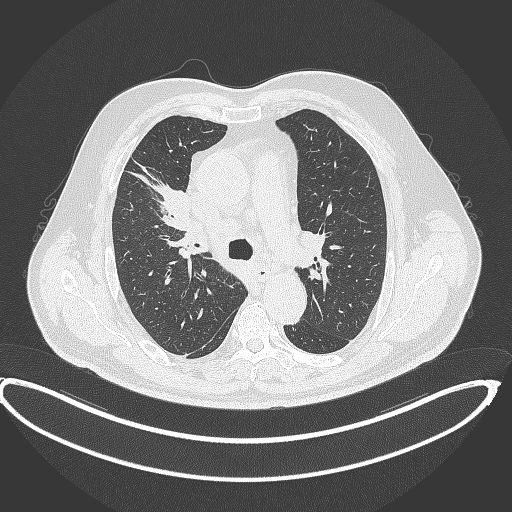
Chest CT, one axial slice. Position 273 of 390 along the scan axis. 120 kVp. Lung window (W 1500 / L -600 HU). 1 mm slice thickness. 512 × 512 image matrix, field of view 448 × 448 mm. Male patient, age 62 years. Case-level facts recorded for this patient, not image findings: clinical TNM (as recorded): T1c N3 M1c.
Outlined on this slice (bounding box drawn by a radiologist):
- lung tumour (recorded histology: adenocarcinoma): bounding box (x1, y1, x2, y2) in pixels: (154, 180, 196, 234)